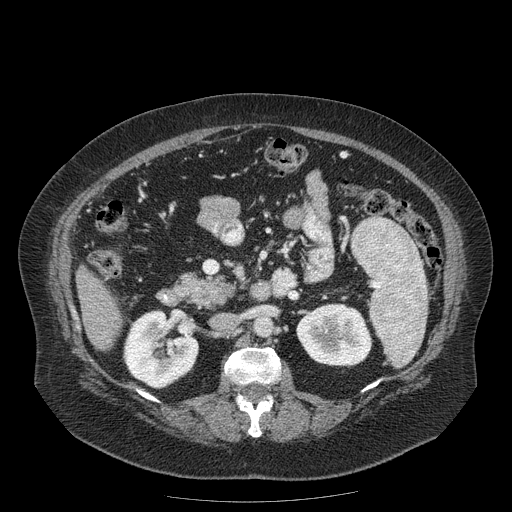
Contrast-enhanced abdominal CT (liver protocol), one axial slice. Slice 59 of 204 in the series (ordered by position). Reconstruction kernel STANDARD. 120 kVp. Soft-tissue window (W 400 / L 40 HU). 512 × 512 image matrix. Case-level facts recorded for this patient, not image findings: diagnosis: hepatocellular carcinoma (patient treated with transarterial chemoembolisation; whether this scan precedes or follows treatment is not stated here); TNM stage (as recorded): Stage-IIIB; Child-Pugh class: A; tumour differentiation: well differentiated; tumour nodularity: uninodular.
Structures marked on this image (semi-automatic segmentation, software-assisted and operator-edited):
- liver parenchyma outside the tumour (the mass and vessels are separate outlines, so this box may not span the whole liver): bounding box <76,264,122,350> (left, top, right, bottom; pixels)